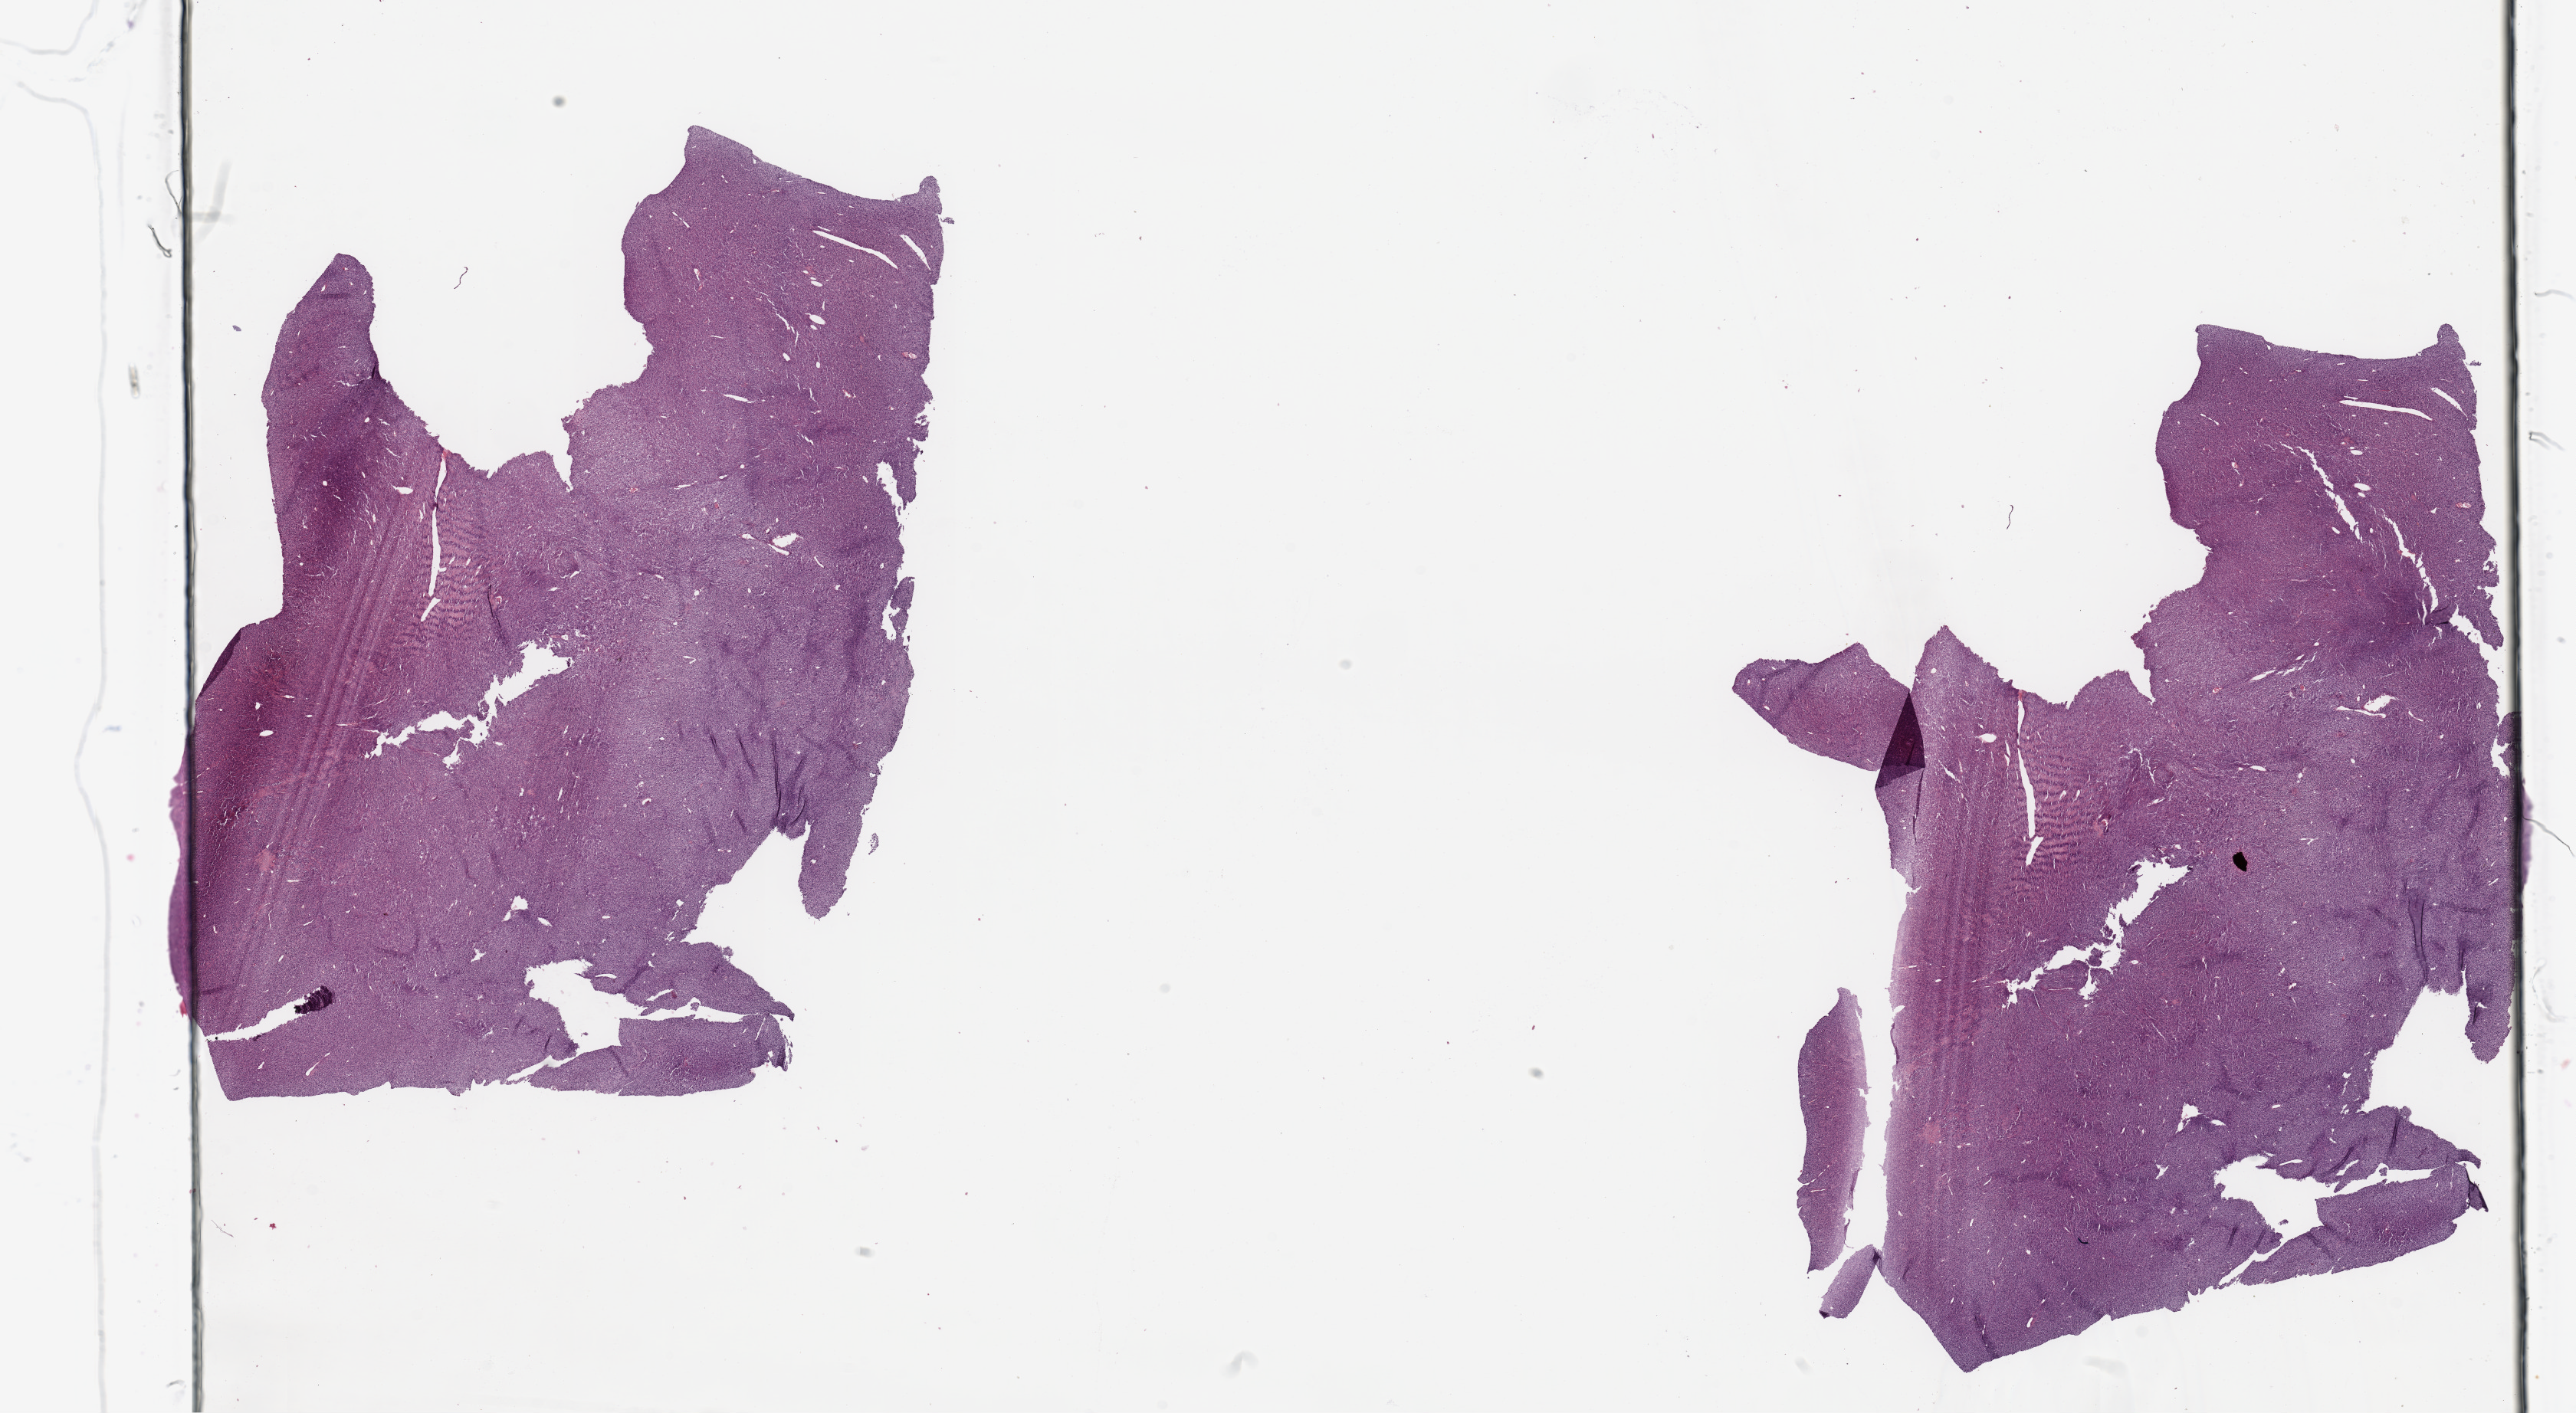
Digitized Hematoxylin and eosin (H&E) stained tissue section (whole slide), a low-resolution overview of the entire scanned area, about 26.6 x 14.6 mm (from a 20x scan). Tumour tissue sample. Patient: female, age 43 years.
Primary tumour site (as recorded): lower extremity. Patient diagnosis (cohort enrolment): sarcoma (site not recorded at cohort level).